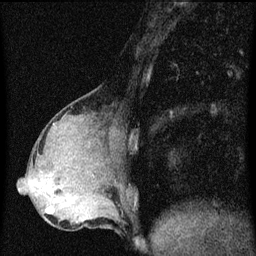
Breast MRI (dynamic contrast-enhanced), one sagittal slice; position 26 of 60 along the scan axis; dynamic contrast-enhanced series, image 2 of 3 at this slice position (ordered by acquisition); 1.5 T; TE 4.2 ms, TR 8 ms; 256 × 256 image matrix, field of view 180 × 180 mm. Patient: female, 49 years.
Outlined on this slice (semi-automatically segmented with operator editing):
- analysis volume of interest (the breast-tissue region the enhancement analysis was run in; not a lesion): bounding box <43,190,88,219> (left, top, right, bottom; pixels)
- tumour enhancement mask (voxels above the 70 % enhancement threshold inside the analysis volume of interest): <46,200,71,213>